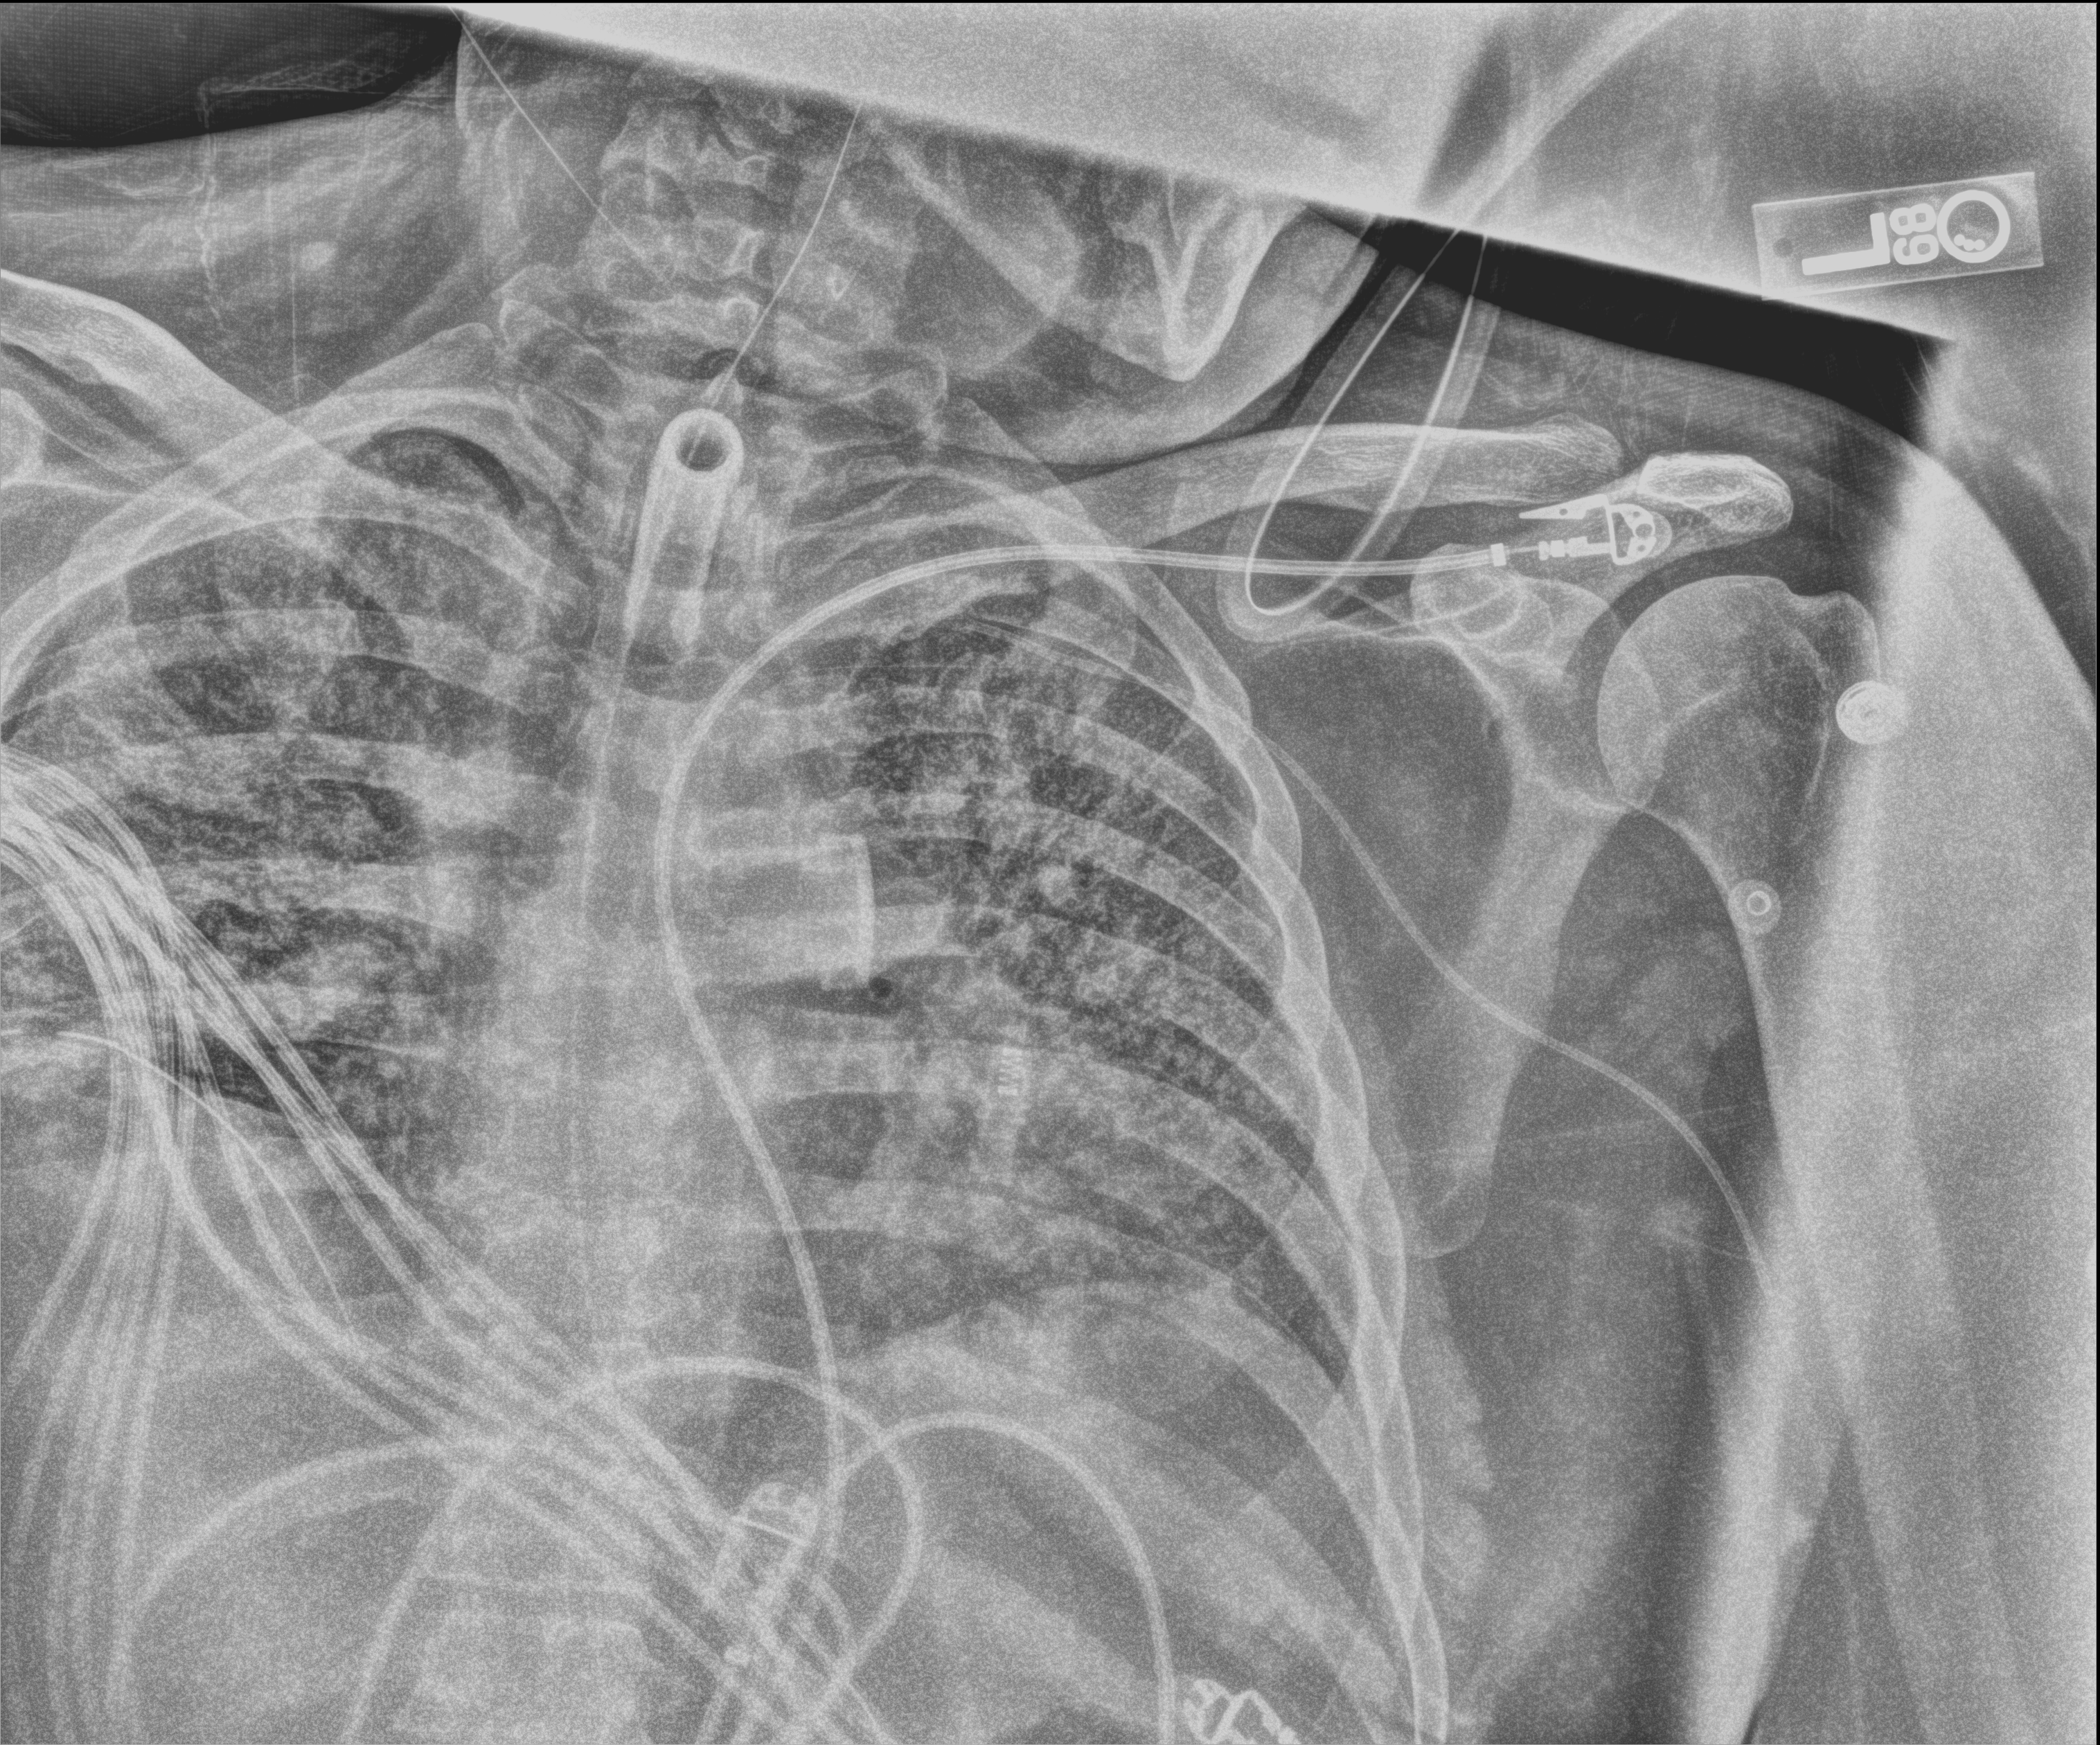
Chest X-ray, anteroposterior (AP) projection. Male patient hospitalised with COVID-19, age 18–59 years.
From the hospital-stay record, not from the radiograph (when in the stay this image was taken is not recorded): mechanically ventilated during this hospital stay: yes; chronic kidney disease (admission record): no; smoking status (admission record): never.